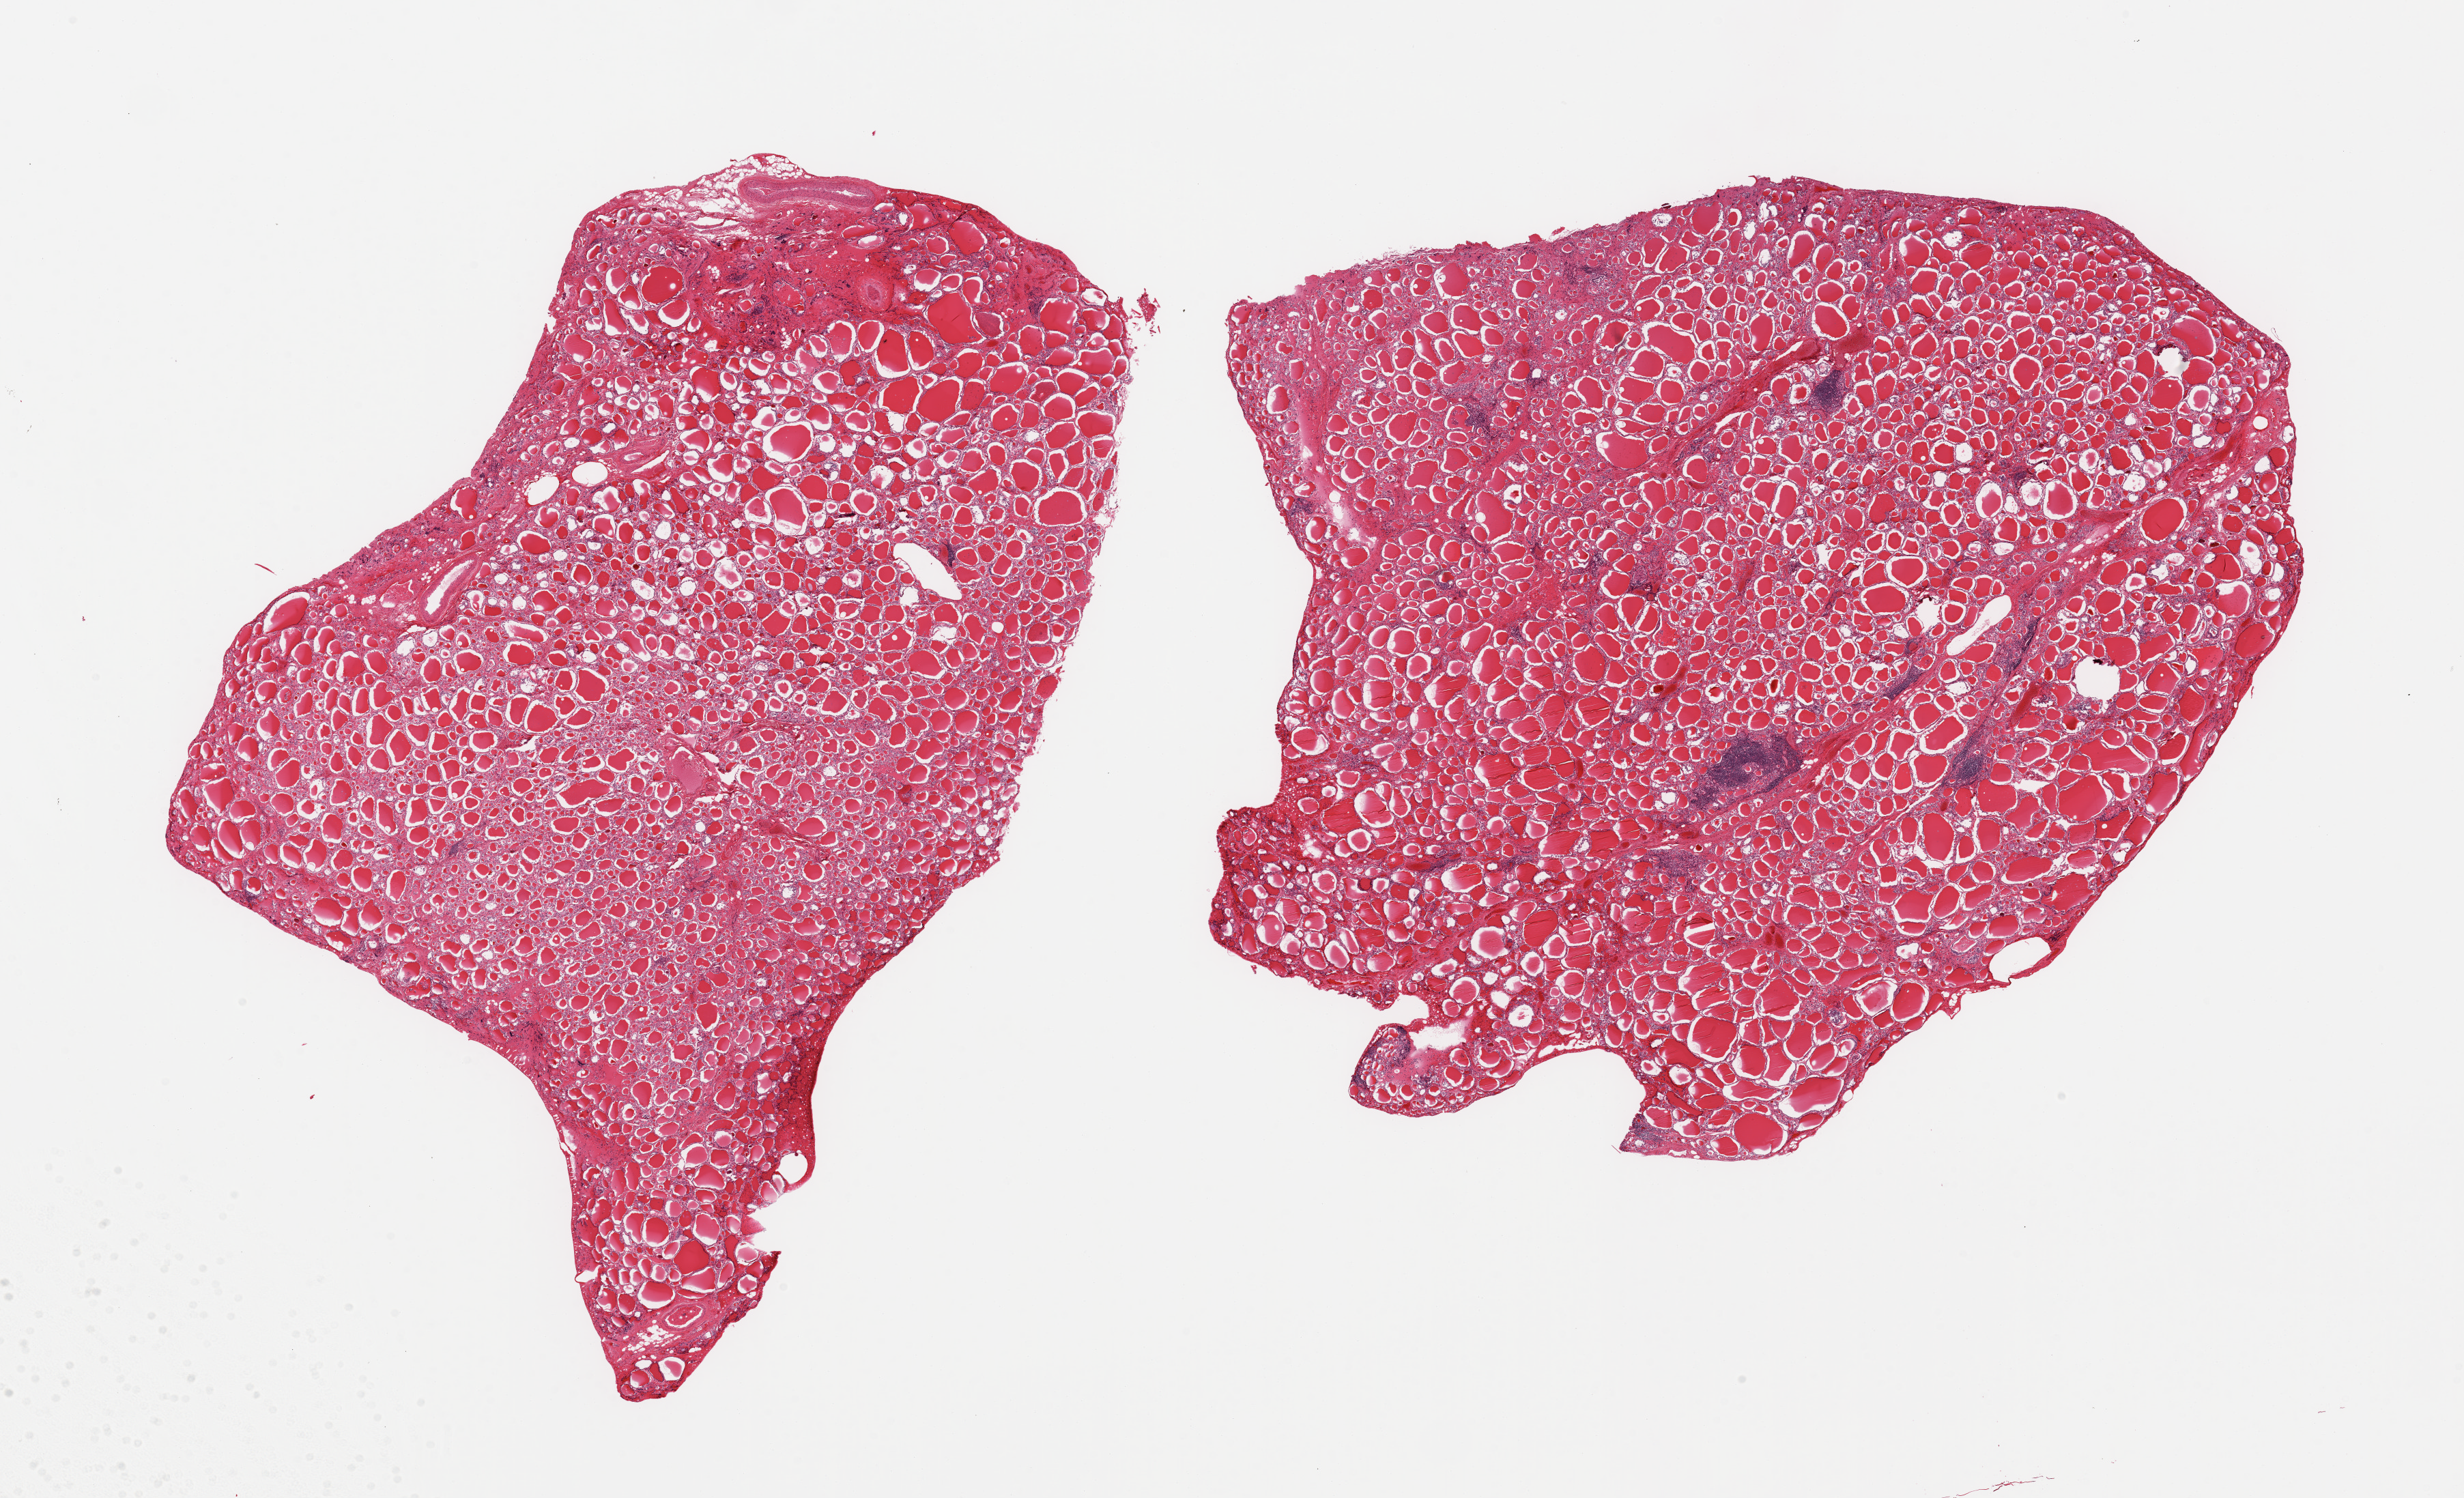
Whole-slide image, haematoxylin and eosin stain — low-resolution overview of the scanned area, about 28.5 x 17.4 mm, PAXgene-fixed paraffin-embedded (PFPE) section, sampled site (target tissue): thyroid, donor tissue sample. Male donor.
Pathologist's review note for this sample: 2 pieces; several foci of lymphocytes consistent with Hashimoto thyroiditis.